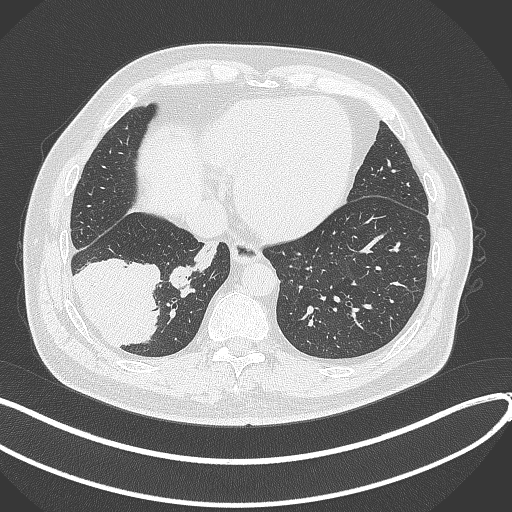
Chest CT, one axial slice. Position 95 of 360 along the scan axis. Reconstruction kernel B70f. 120 kVp. Lung window (W 1500 / L -600 HU). 512 × 512 image matrix. Patient: male, 59 years.
Outlined on this slice (rectangle marked by the reading radiologist):
- lung tumour (recorded histology: adenocarcinoma): bounding box [x1, y1, x2, y2] px = [72, 252, 163, 350]